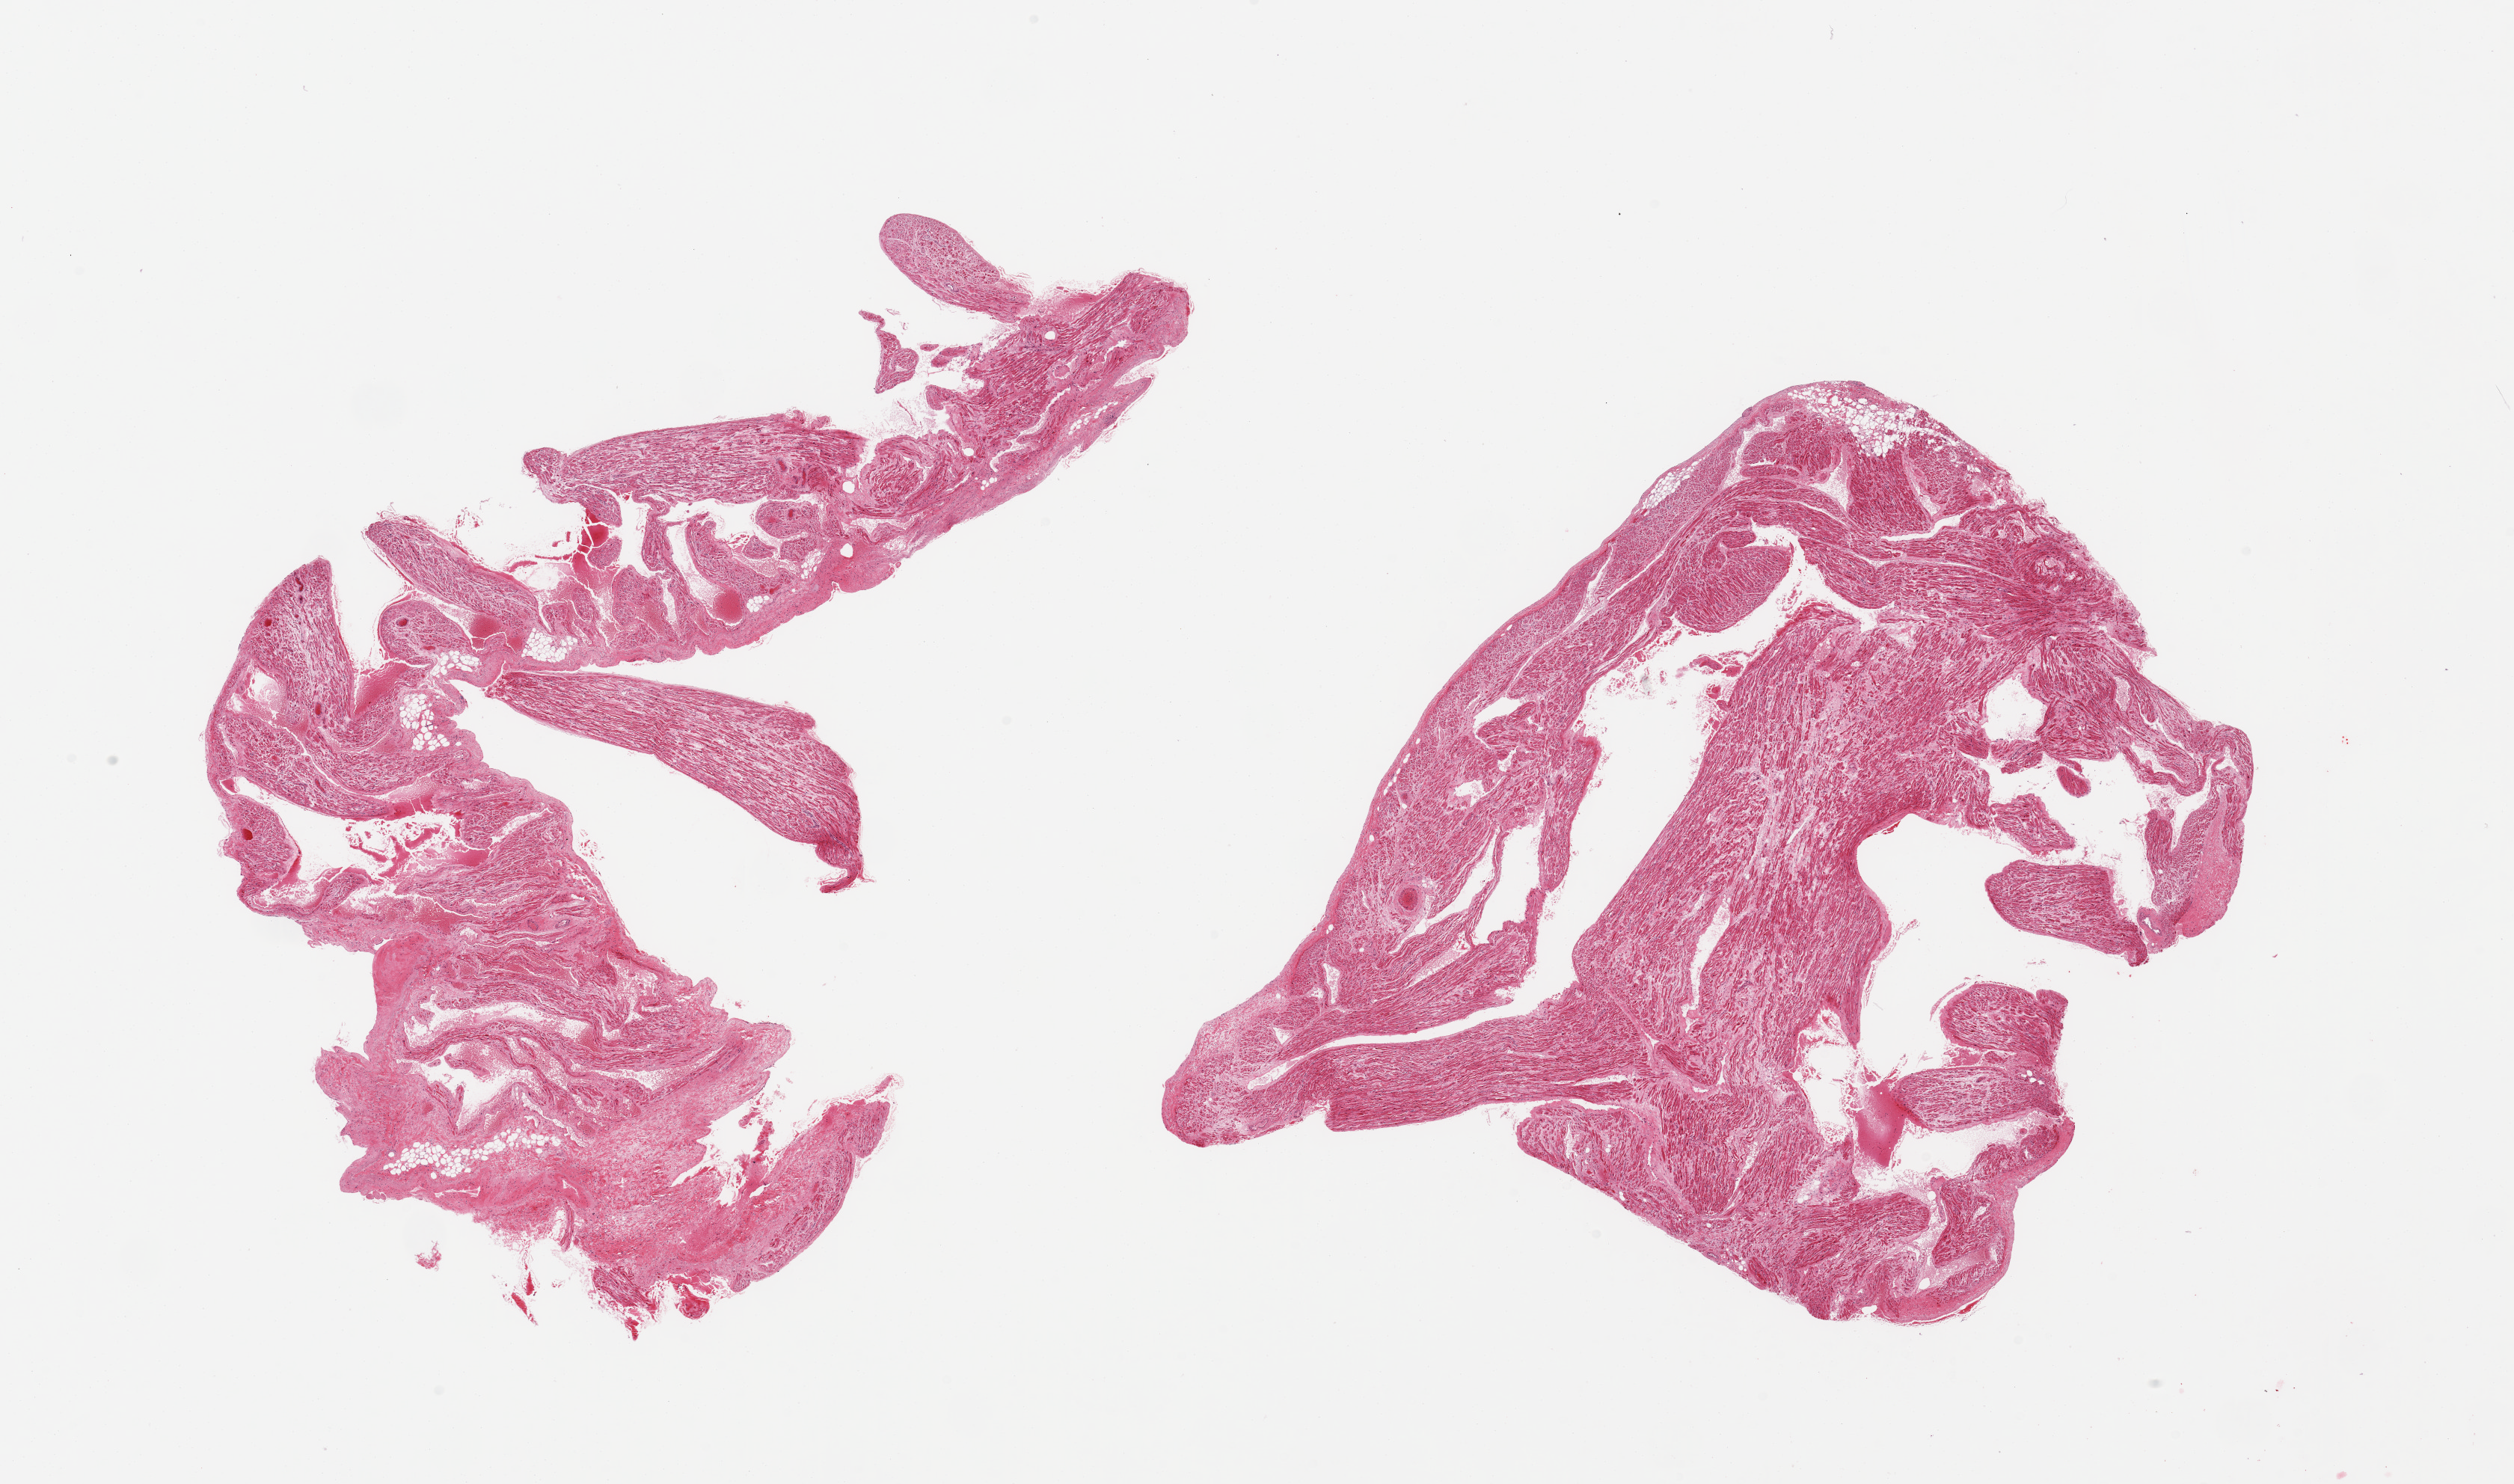
Digitized hematoxylin and eosin (H&E)-stained section, whole scanned area (about 26.6 x 15.7 mm) shown as a low-resolution overview. PAXgene-fixed paraffin-embedded (PFPE) section. Sampled site (target tissue): auricular appendage. Donor tissue sample. Donor sex: male.
Reviewer comment on this tissue sample: 2 pieces, no abnormalities.